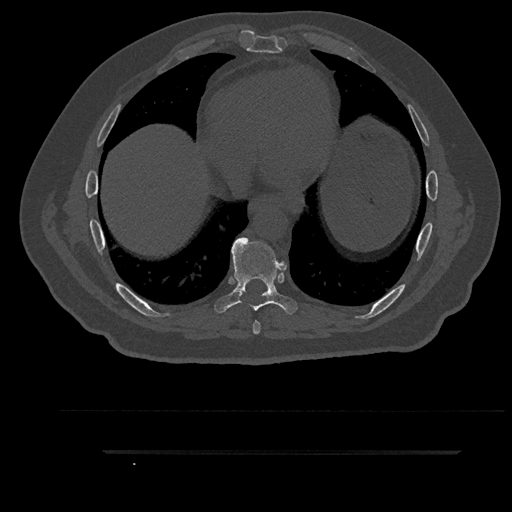
CT including the spine, one axial slice. Position 482 of 797 along the scan axis. Reconstruction kernel Br40s/3. Bone window (W 1800 / L 400 HU). 0.5 mm slice thickness. 512 × 512 image matrix, field of view 432 × 432 mm. Male patient, age 63 years. Case-level facts recorded for this patient, not image findings: primary cancer: renal.
Outlined on this slice (semi-automatically segmented with operator editing):
- T7 vertebra: bounding box (x1, y1, x2, y2) in pixels: (253, 321, 261, 334)
- T8 vertebra: (215, 237, 298, 315)